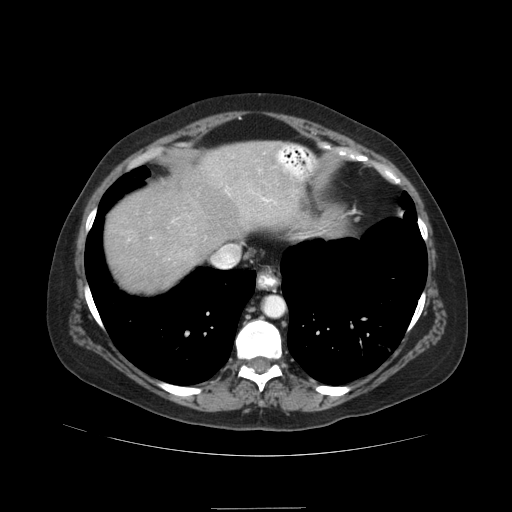
Contrast-enhanced abdominal CT (liver protocol), one axial slice; position 76 of 89 along the scan axis; soft-tissue window (W 400 / L 40 HU); 2.5 mm slice thickness; 512 × 512 image matrix. From the clinical record (not read from this slice): diagnosis: hepatocellular carcinoma (patient treated with transarterial chemoembolisation; whether this scan precedes or follows treatment is not stated here); TNM stage (as recorded): Stage-IIIB; Child-Pugh class: A; tumour nodularity: multinodular.
Structures marked on this image (semi-automatically segmented with operator editing):
- liver parenchyma outside the tumour (the mass and vessels are separate outlines, so this box may not span the whole liver): bounding box [x1, y1, x2, y2] px = [104, 142, 302, 292]
- liver vessels: [229, 194, 270, 202]